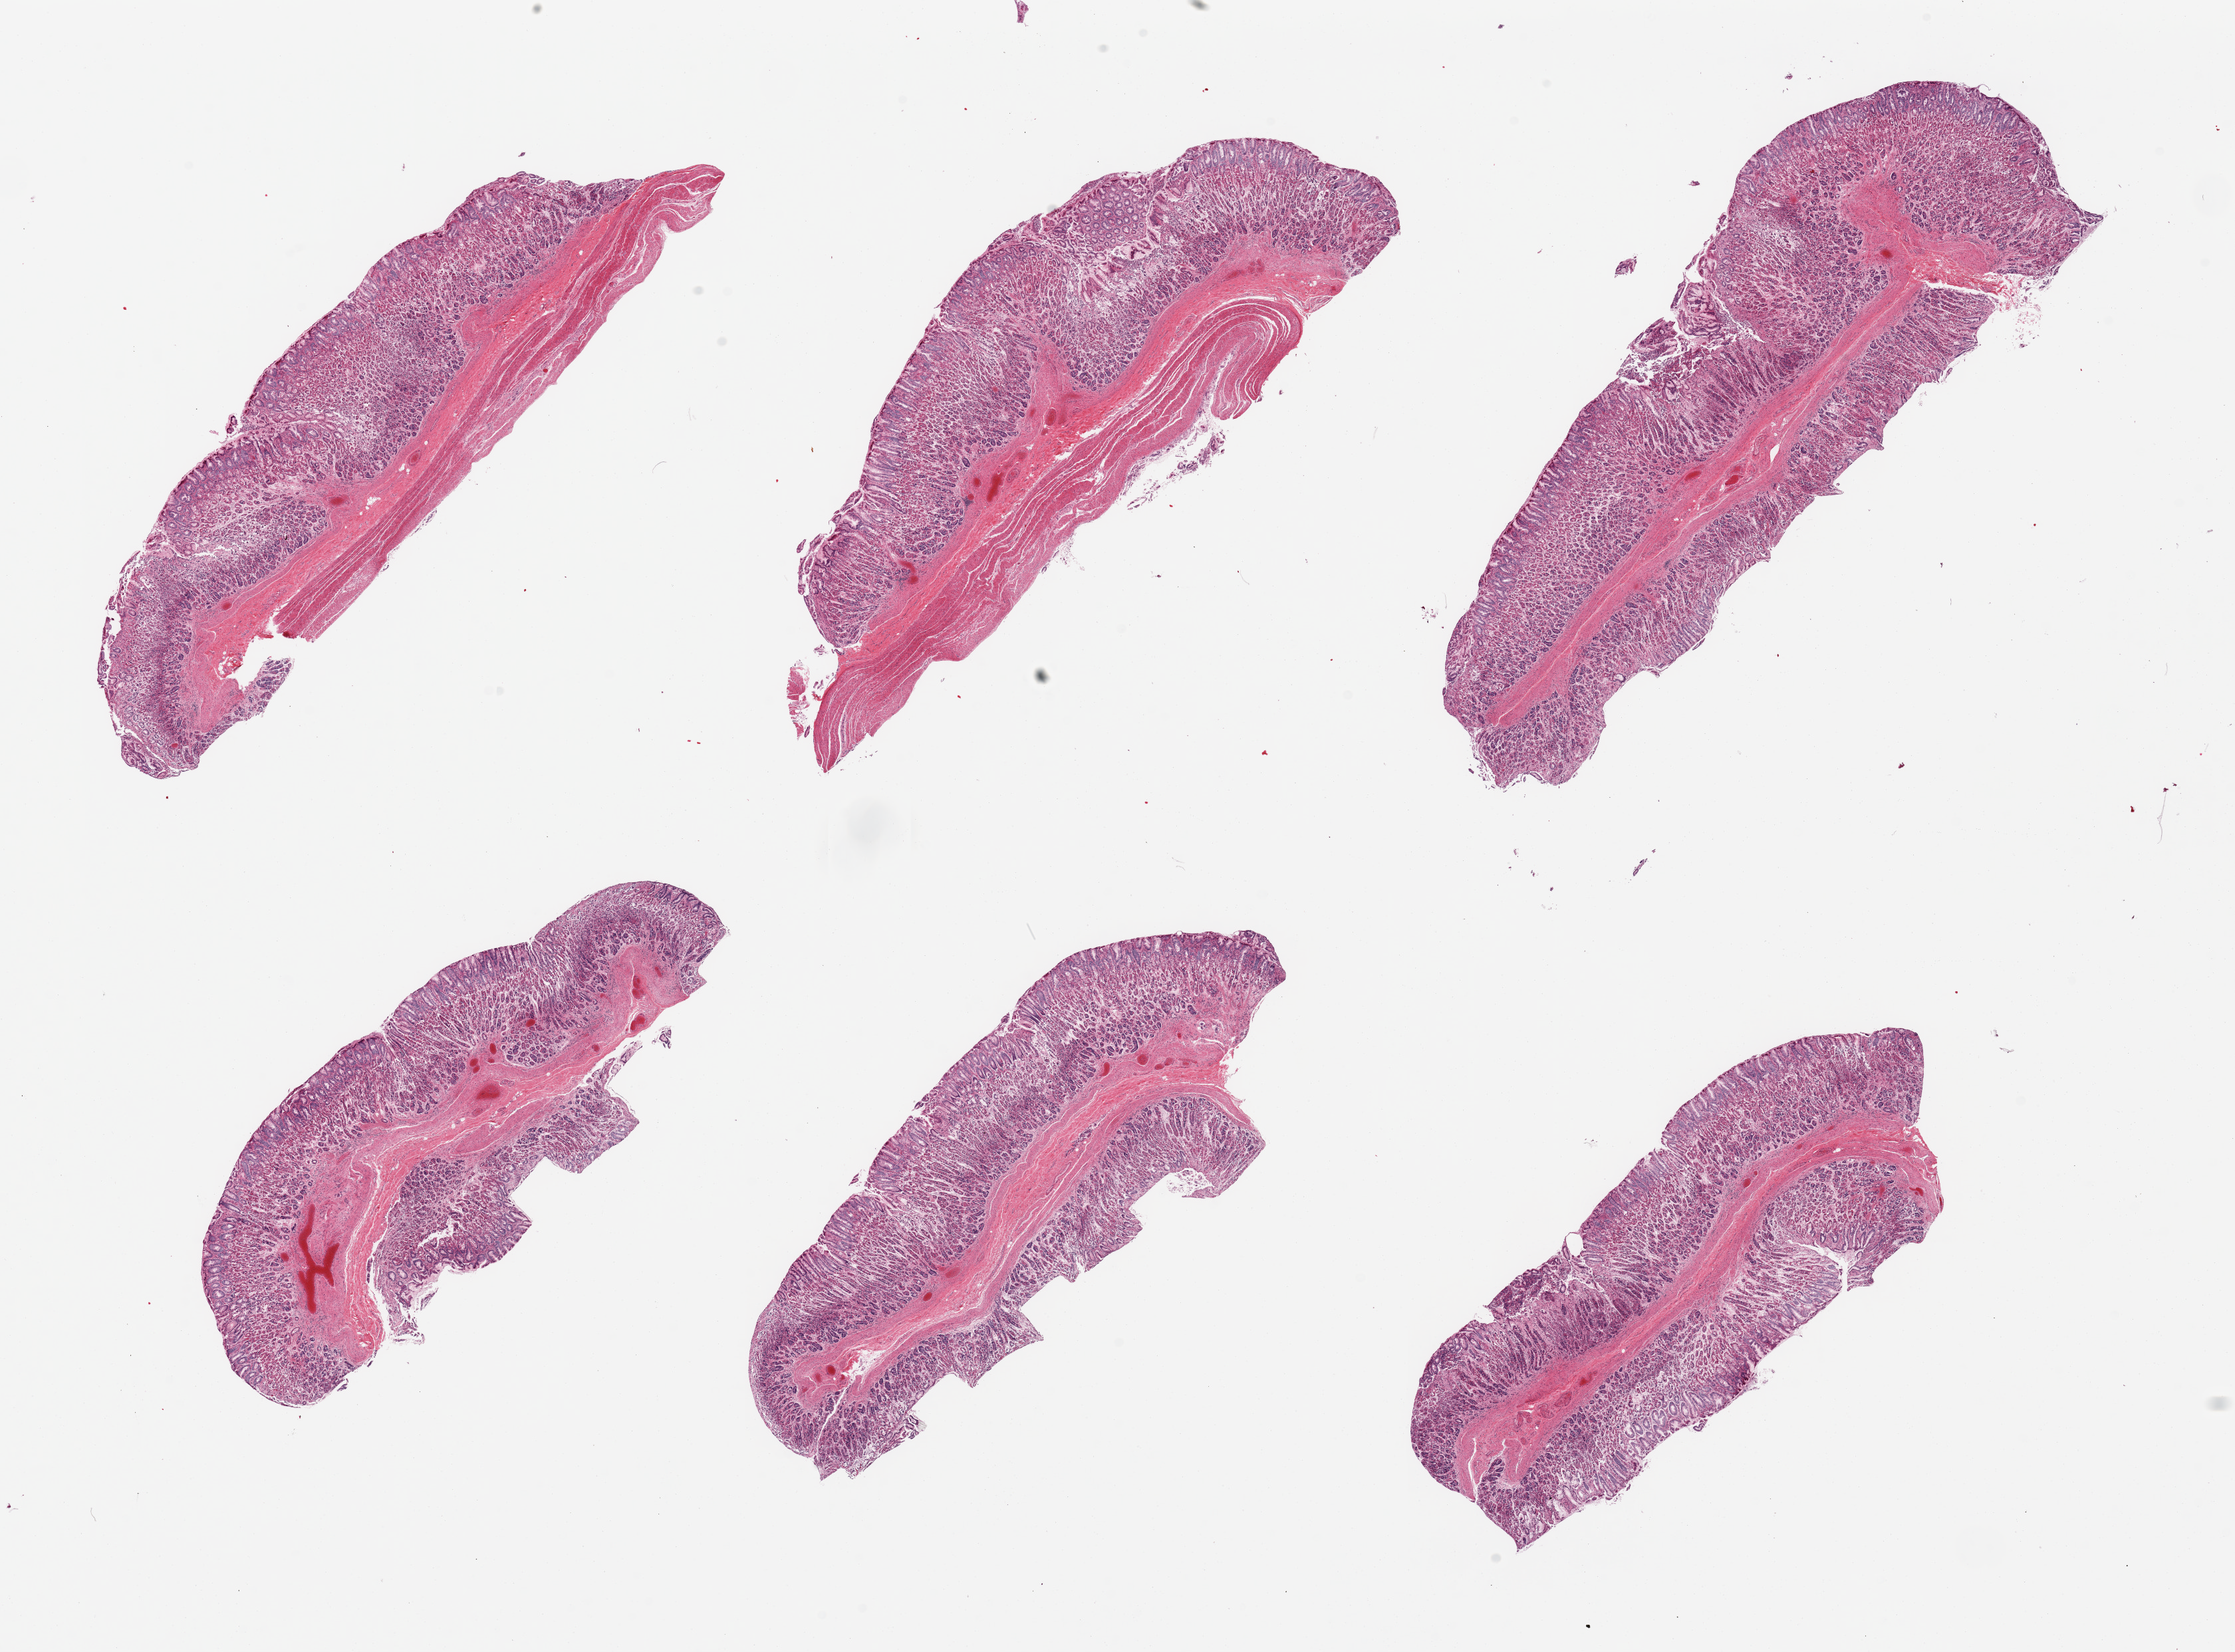
H&E whole-slide image, brightfield, low-resolution overview of the scanned area, about 26.6 x 19.7 mm (acquisition: 20x scan), PAXgene-fixed paraffin-embedded (PFPE) section, sampled site (target tissue): stomach, donor tissue sample. Female donor.
Review note (as recorded): 6 pieces, mucosa is ~50-80% thickness, moderately-markedly autolyzed.